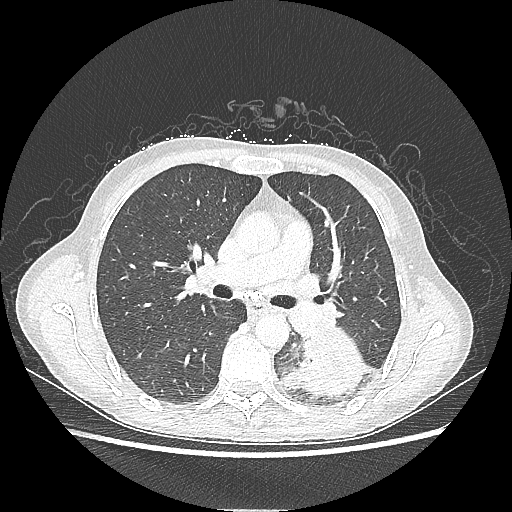
Chest CT, one axial slice. Position 130 of 220 along the scan axis. Lung window (W 1500 / L -600 HU). 1.25 mm slice thickness. 512 × 512 image matrix. Patient: female, 53 years. Case-level facts recorded for this patient, not image findings: clinical TNM (as recorded): T3 N0 M0.
Outlined on this slice (rectangle marked by the reading radiologist):
- lung tumour (recorded histology: adenocarcinoma): bounding box (x1, y1, x2, y2) in pixels: (278, 331, 376, 400)